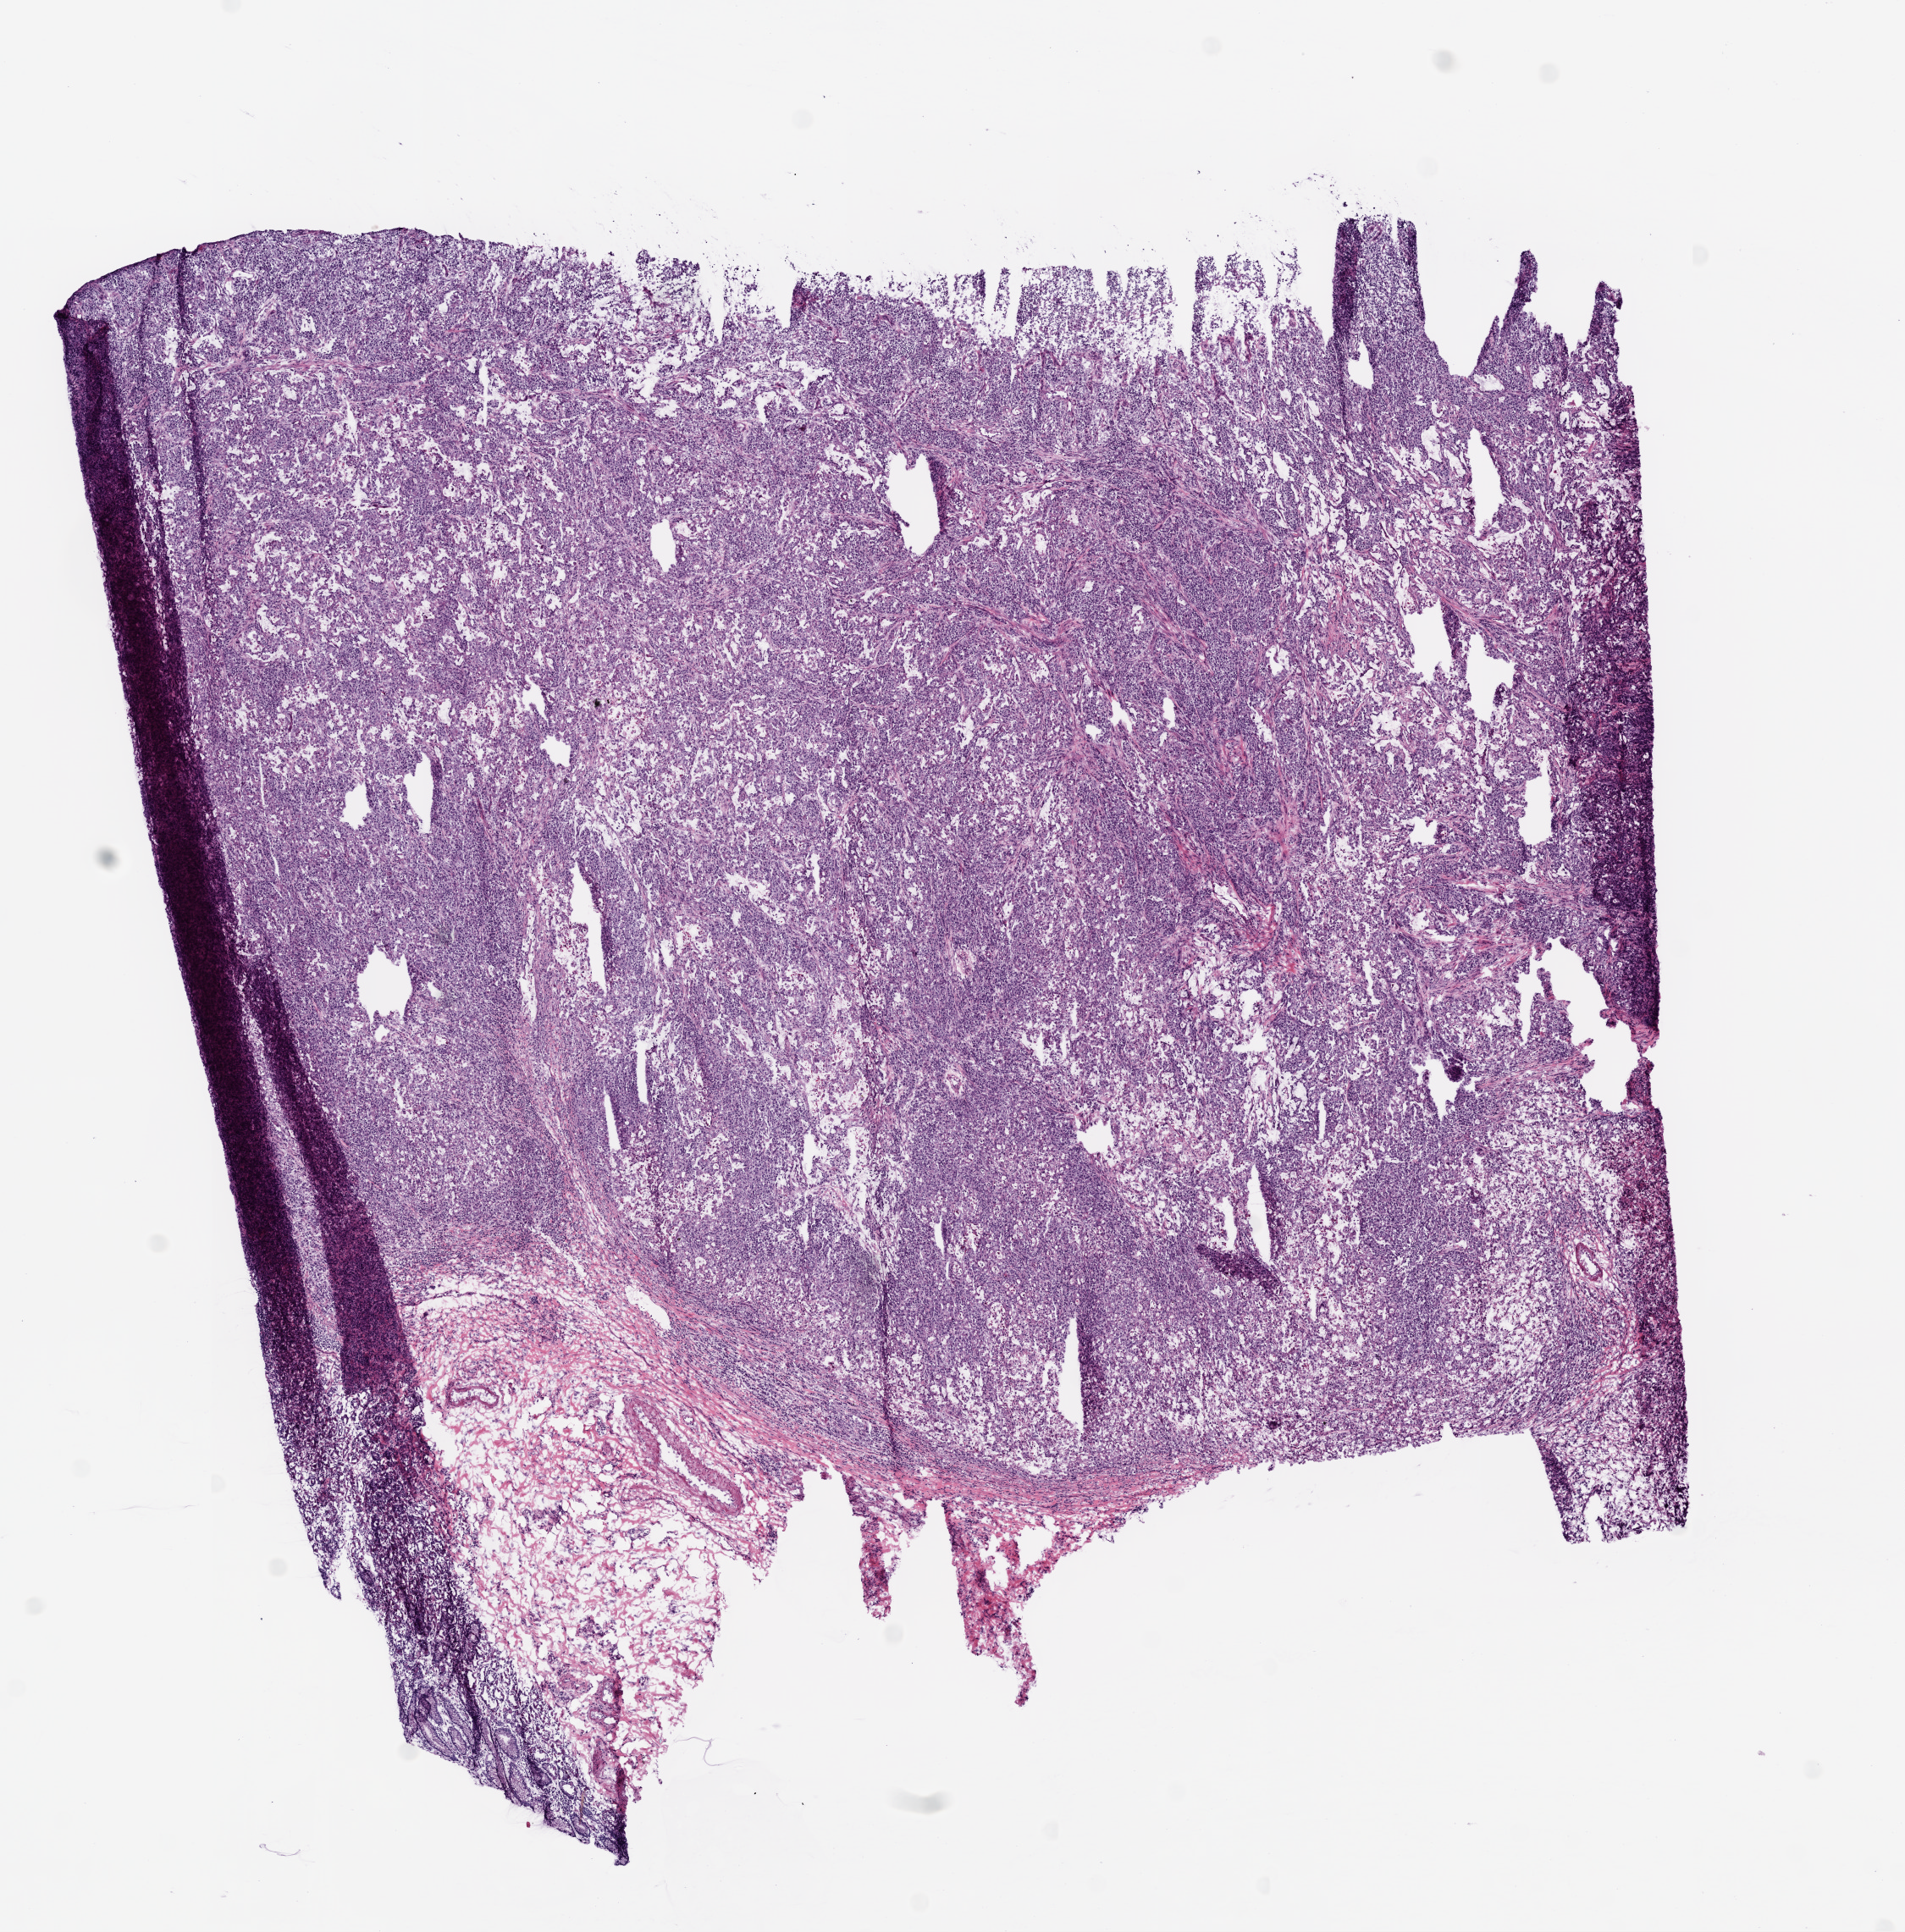
Hematoxylin and eosin (H&E) stained whole-slide image — a low-resolution overview of the entire scanned area, about 9.0 x 9.2 mm (slide scanned at 20x); frozen section from the bottom of the tissue portion; sample: primary tumour, stomach. Female patient; age at initial diagnosis 69 years. Histologic grade: G3 (poorly differentiated). Slide review estimates, as recorded: tumour cells 80%, tumour nuclei 70%, normal cells 0%, stromal cells 10%, necrosis 10%.
• diagnosis: Carcinoma, diffuse type (gastric antrum)
• AJCC pathologic stage: IV
• lymph nodes positive (case pathology): 21 of 27 examined